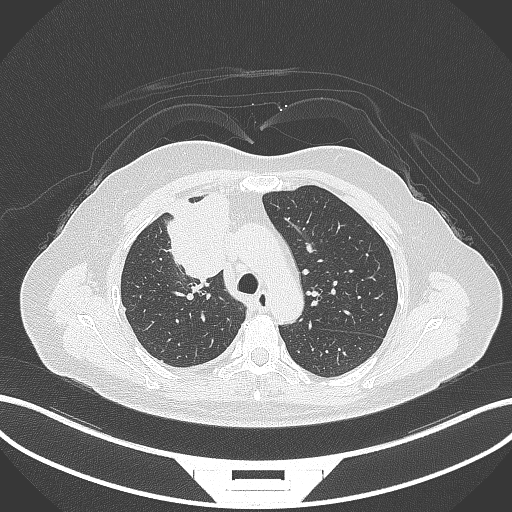
Chest CT, one axial slice; position 206 of 305 along the scan axis; reconstruction kernel B70f; lung window (W 1500 / L -600 HU); 1 mm slice thickness; 512 × 512 image matrix. Female patient, age 52 years. From the clinical record (not read from this slice): clinical TNM (as recorded): T3 N1 M1.
Outlined on this slice (rectangle marked by the reading radiologist):
- lung tumour (recorded histology: adenocarcinoma): bounding box <163,194,231,279> (left, top, right, bottom; pixels)